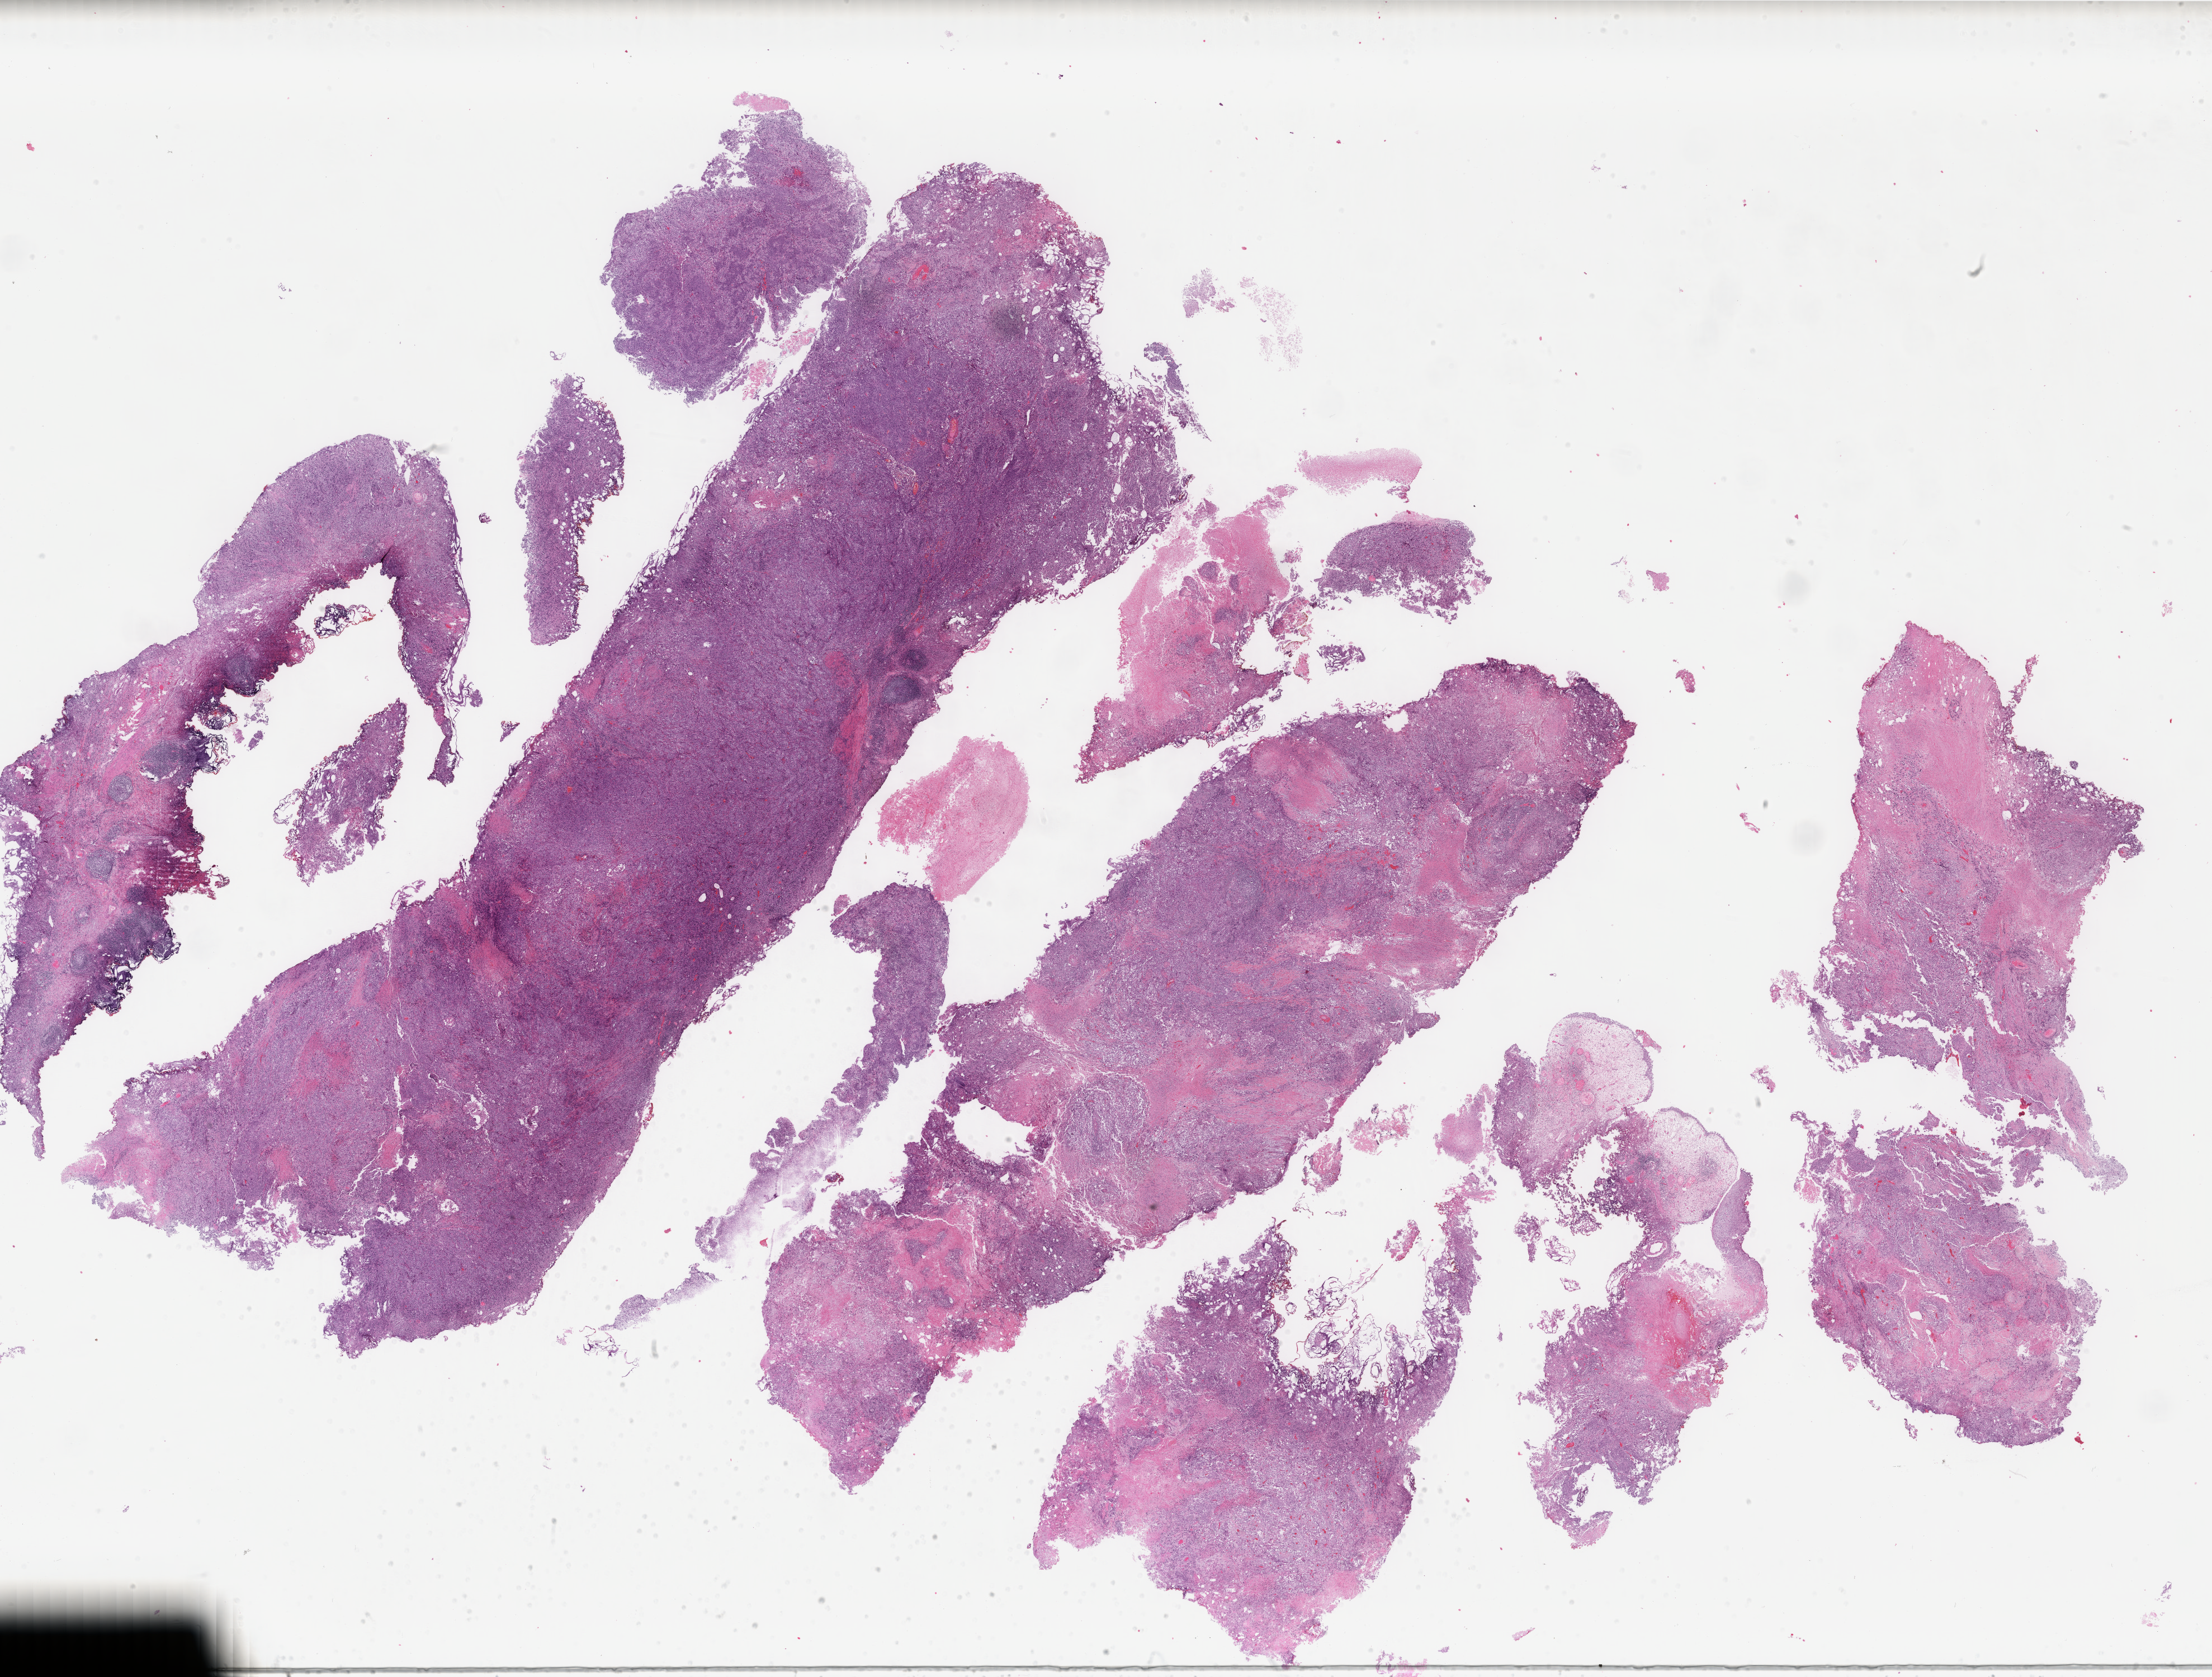
Whole-slide histology image, H&E-stained — low-resolution overview of the scanned area, about 31.4 x 23.8 mm (slide scanned at 40x); FFPE section; primary tumour sample from the bladder. Male patient; age at initial diagnosis 50 years. Histologic grade: high grade.
• AJCC pathologic stage: II (6th edition)
• pathologic diagnosis: Transitional cell carcinoma